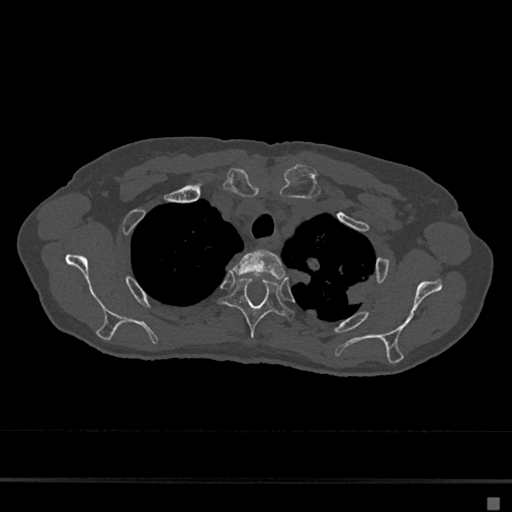
CT including the spine, one axial slice. Slice 547 of 797 in the series (ordered by position). Reconstruction kernel Br40s/3. 120 kVp. Bone window (W 1800 / L 400 HU). 0.5 mm slice thickness. 512 × 512 image matrix, field of view 360 × 360 mm. Patient: female, 68 years. From the clinical record (not read from this slice): primary cancer: renal.
Annotated regions visible in this slice (semi-automatic segmentation, software-assisted and operator-edited):
- T2 vertebra: bounding box [x1, y1, x2, y2] px = [232, 249, 286, 280]
- T3 vertebra: [220, 278, 294, 339]